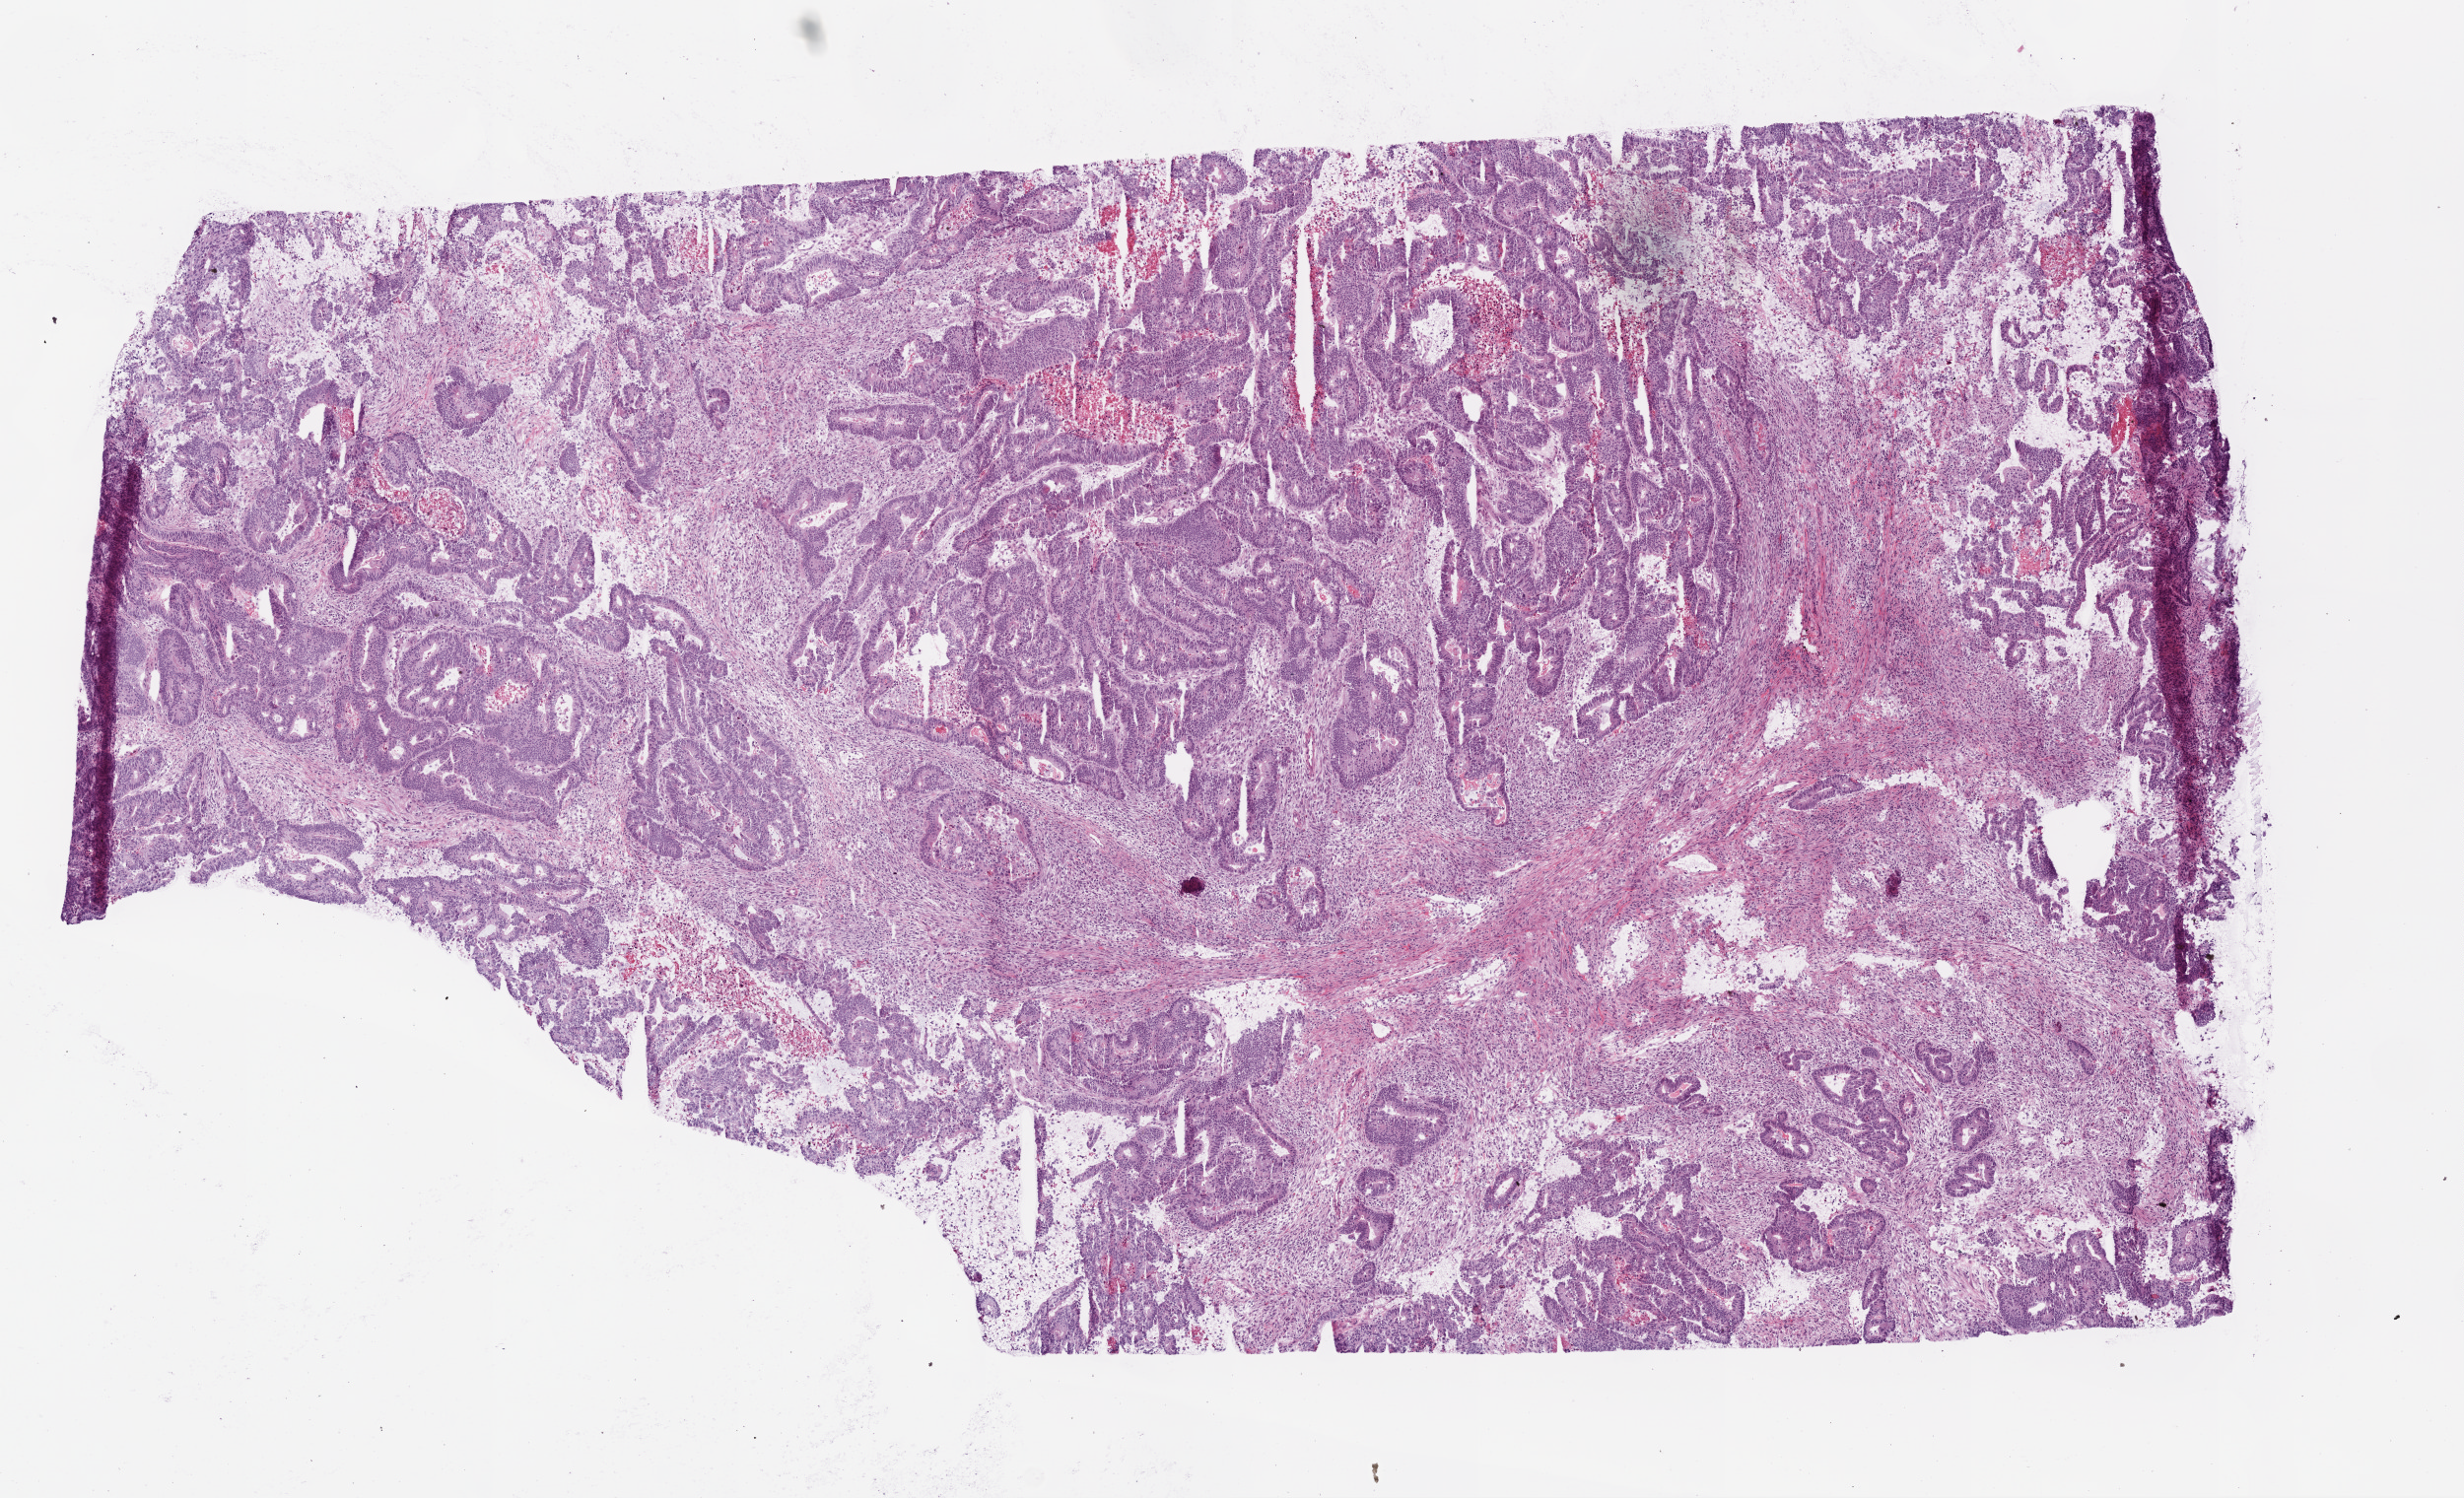
Digitized Hematoxylin and eosin (H&E) stained tissue section (whole slide) — shown as a low-resolution overview of the whole scanned area (about 10.0 x 6.1 mm, from a 20x scan), frozen section from the top of the tissue portion, sample: primary tumour, colon. Male, age 79 years at initial diagnosis. Slide review estimates, as recorded: tumour cells 60%, tumour nuclei 60%, normal cells 0%, stromal cells 30%, necrosis 10%.
Diagnosis: Adenocarcinoma, NOS. Lymph nodes positive (case pathology): 0 of 19 examined. AJCC pathologic stage: IIA. TNM: T3 N0 M0.